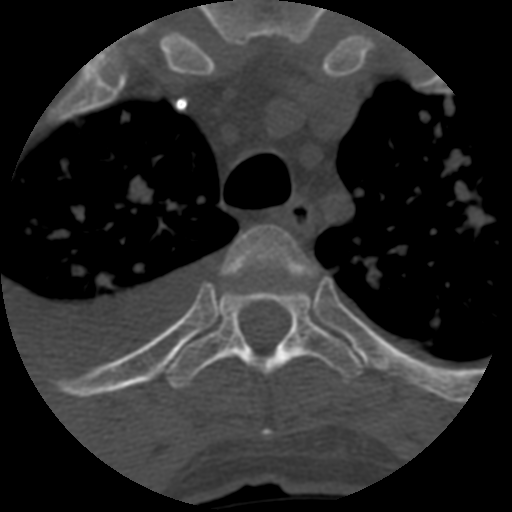
CT including the spine, one axial slice. Slice 477 of 708 in the series (ordered by position). Reconstruction kernel STANDARD. 120 kVp. One of 3 acquisitions stored at this slice position. Bone window (W 1800 / L 400 HU). 1.25 mm slice thickness. 512 × 512 image matrix, field of view 160 × 160 mm. Patient age 55 years. From the clinical record (not read from this slice): primary cancer: colon; vertebrae with lytic lesions (as recorded): T12, L1, L5.
Outlined on this slice (semi-automatic segmentation, software-assisted and operator-edited):
- T3 vertebra: bounding box (x1, y1, x2, y2) in pixels: (223, 225, 315, 433)
- T4 vertebra: (165, 272, 364, 389)